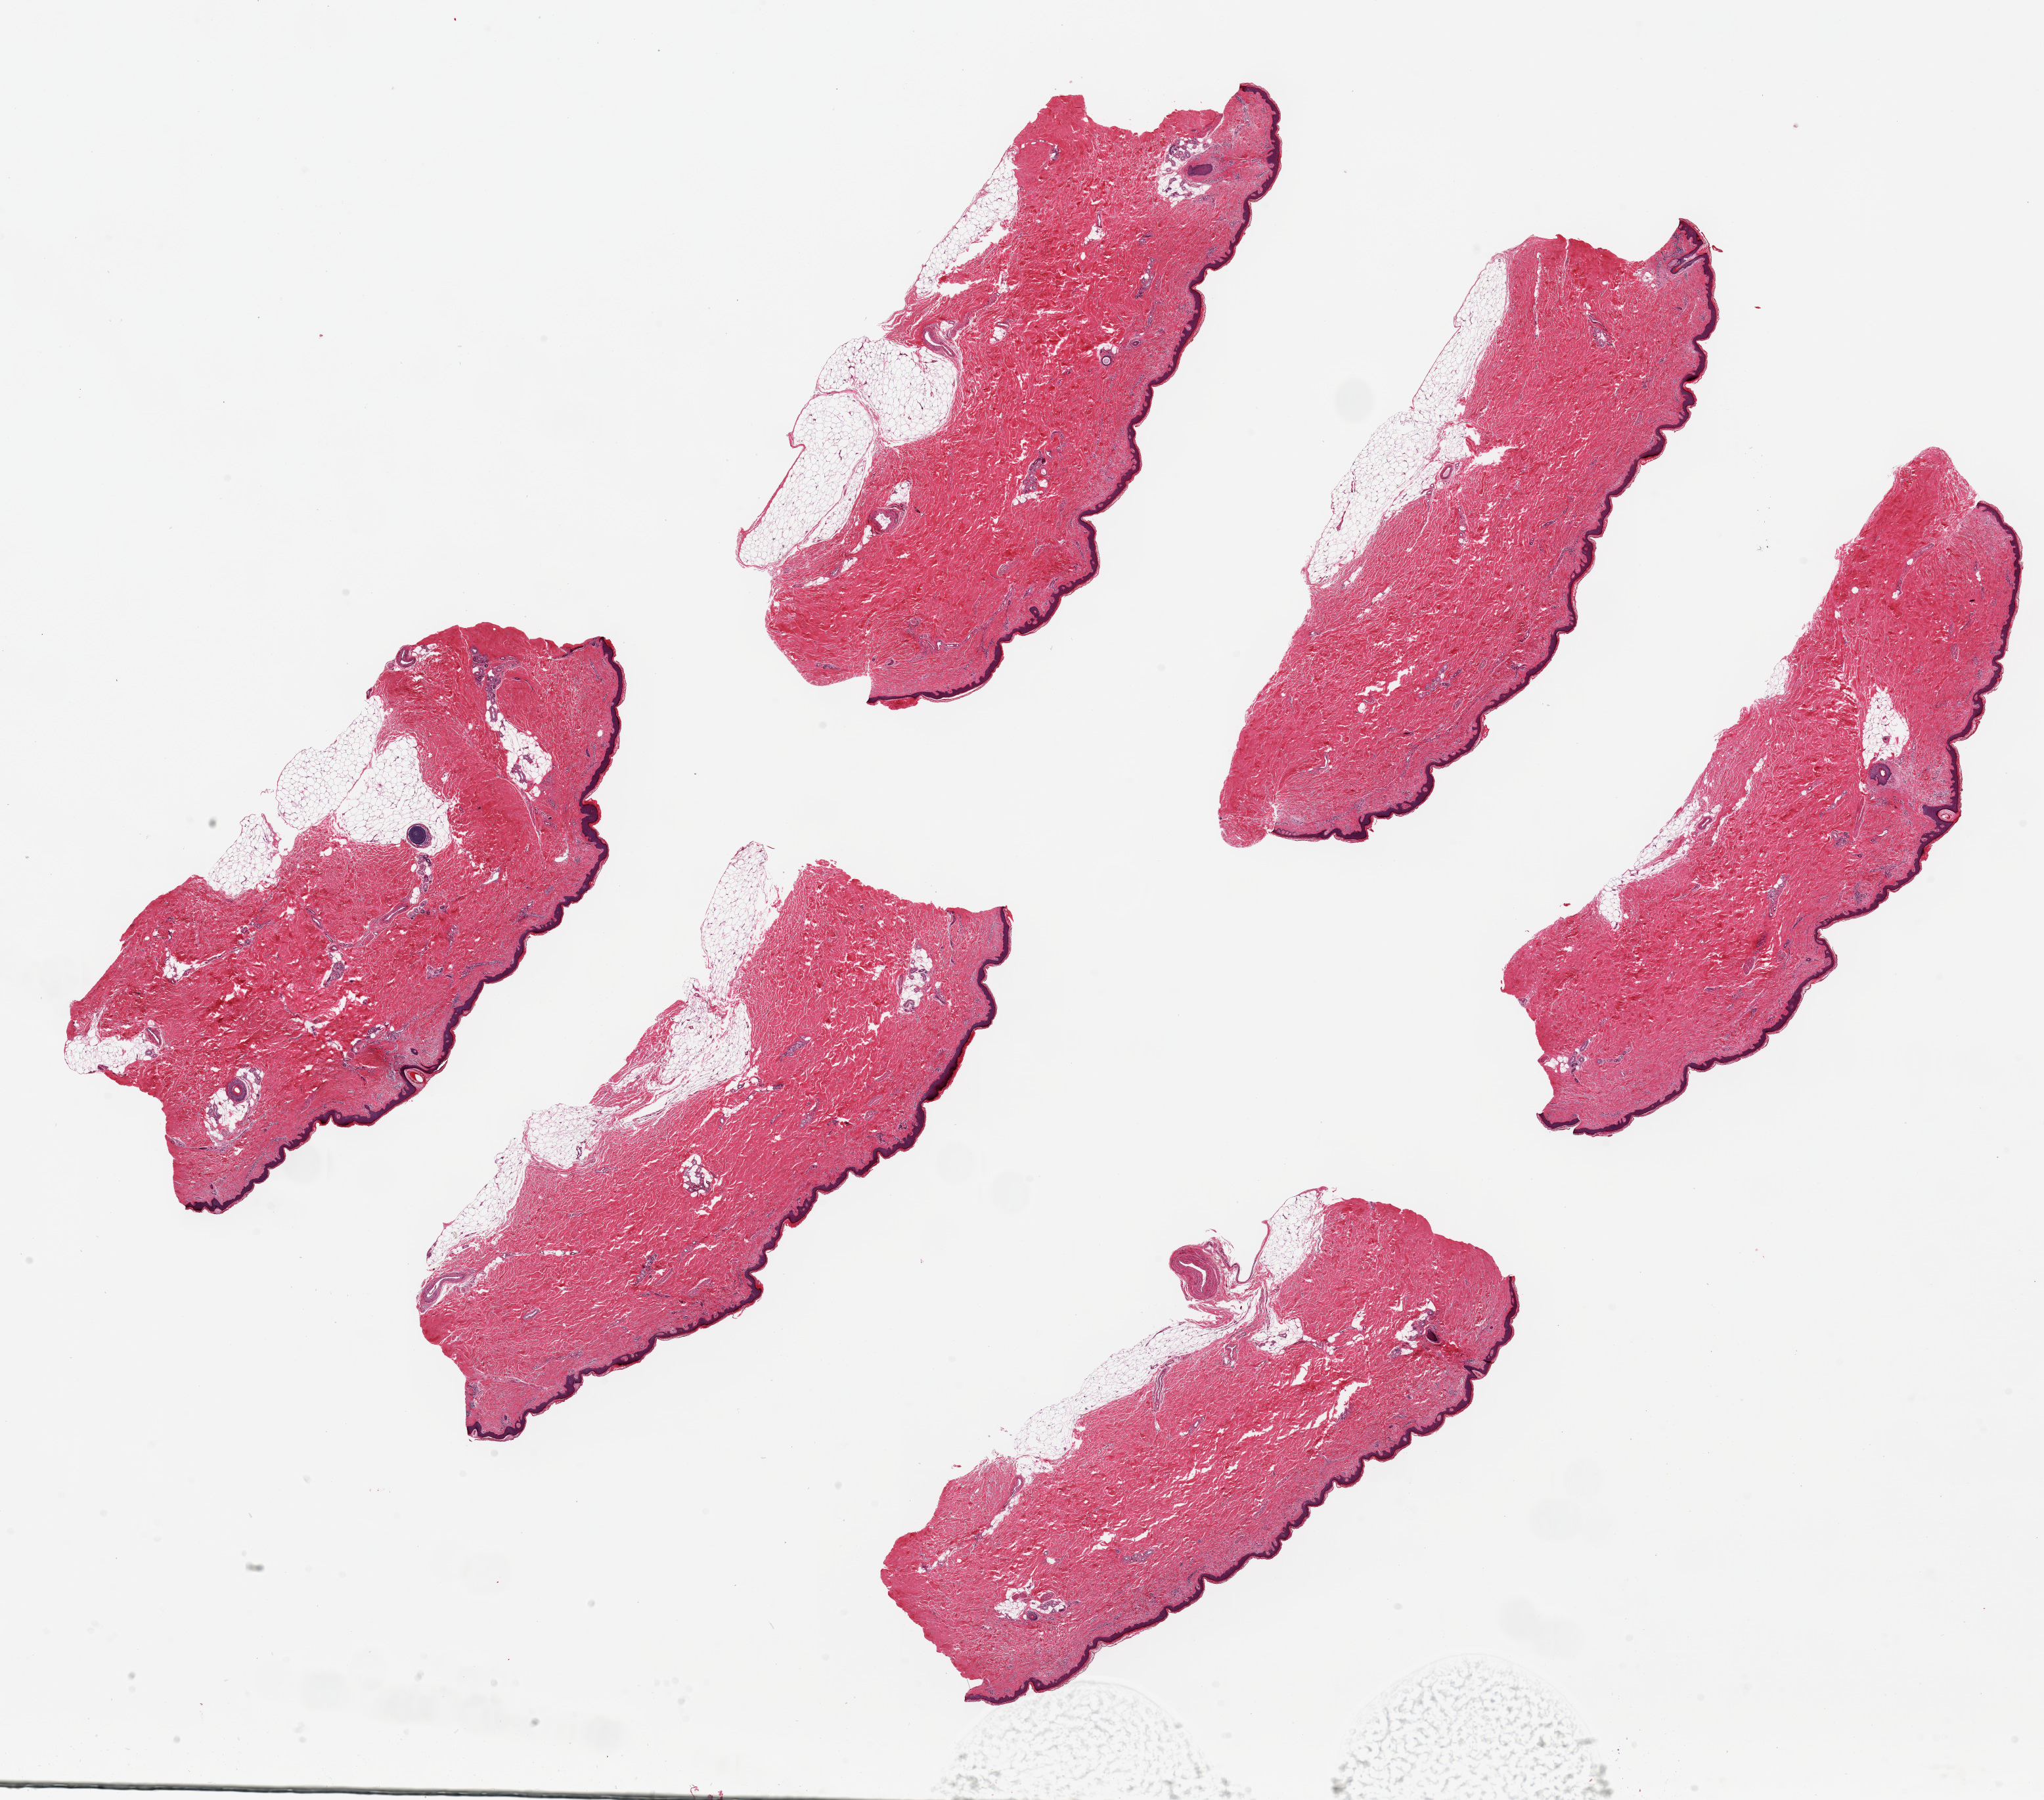
Hematoxylin and eosin (H&E) whole-slide image, brightfield — a low-resolution overview of the entire scanned area, about 24.6 x 21.7 mm; PAXgene-fixed paraffin-embedded (PFPE) section; sampled site (target tissue): skin of lower leg; donor tissue sample.
• reviewer comment on this tissue sample: 6 ~8.5x2.5mm pieces; squamous epithelium is ~1-3% of thickness